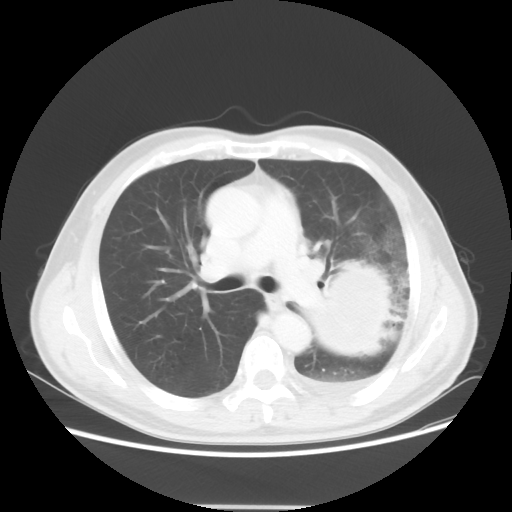
Chest CT, one axial slice. Slice 33 of 53 in the series (ordered by position). 100 kVp. Lung window (W 1500 / L -600 HU). 5 mm slice thickness. 512 × 512 image matrix, field of view 391 × 391 mm. Patient: male, 60 years. Case-level facts recorded for this patient, not image findings: clinical TNM (as recorded): T4 N1 M1a; histopathological grade: G3.
Structures marked on this image (bounding box drawn by a radiologist):
- lung tumour (recorded histology: large cell carcinoma): box from (x=308, y=262) to (x=398, y=362) px